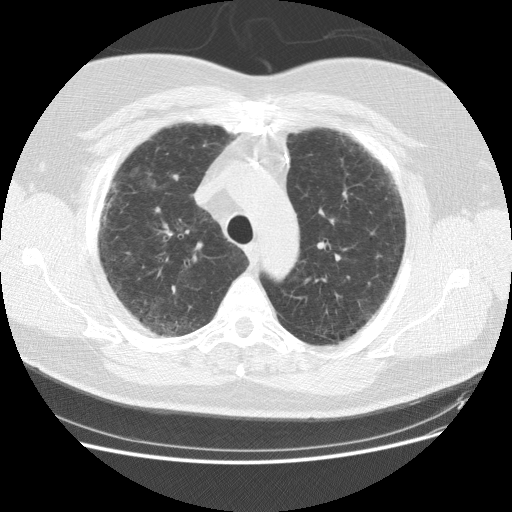
Chest CT (low-dose screening protocol), one axial image. Baseline annual screen. Lung window (W 1500 / L -600 HU). 2.5 mm slice thickness. 512 × 512 image matrix, field of view 378 × 378 mm. Male, age 59 years at enrolment.
Expert-annotated lung lesion, bounding box <90,166,142,228> (left, top, right, bottom; pixels). The screening reader recorded 2 non-calcified nodules or masses ≥4 mm on this exam; which of them this box marks is not recorded. Official screen result: positive, change unspecified: nodule(s) >= 4 mm or enlarging nodule(s), mass(es), or other non-specific abnormalities suspicious for lung cancer. Participant outcome: lung cancer diagnosed 338 days after this screen — adenocarcinoma, NOS, right upper lobe, right middle lobe, moderately differentiated (G2), stage IA (AJCC 6th edition), 13 mm at pathology.